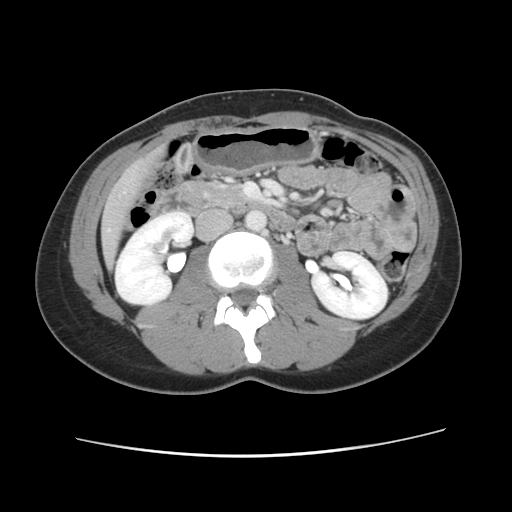
Contrast-enhanced abdominal CT, one axial slice; slice 27 of 134 in the series (ordered by position); 120 kVp; intravenous contrast given; soft-tissue window (W 400 / L 40 HU); 512 × 512 image matrix, field of view 339 × 339 mm. Female patient, age 33 years. From the clinical record (not read from this slice): diagnosis: colorectal cancer liver metastases, imaged before liver resection; multiple liver metastases: yes; largest metastasis: 4.5 cm.
Outlined on this slice (outlined manually by an expert reader):
- liver: box from (x=101, y=152) to (x=164, y=266) px
- planned liver remnant (the part of the liver to remain after resection): (x=103, y=245)–(x=114, y=267)